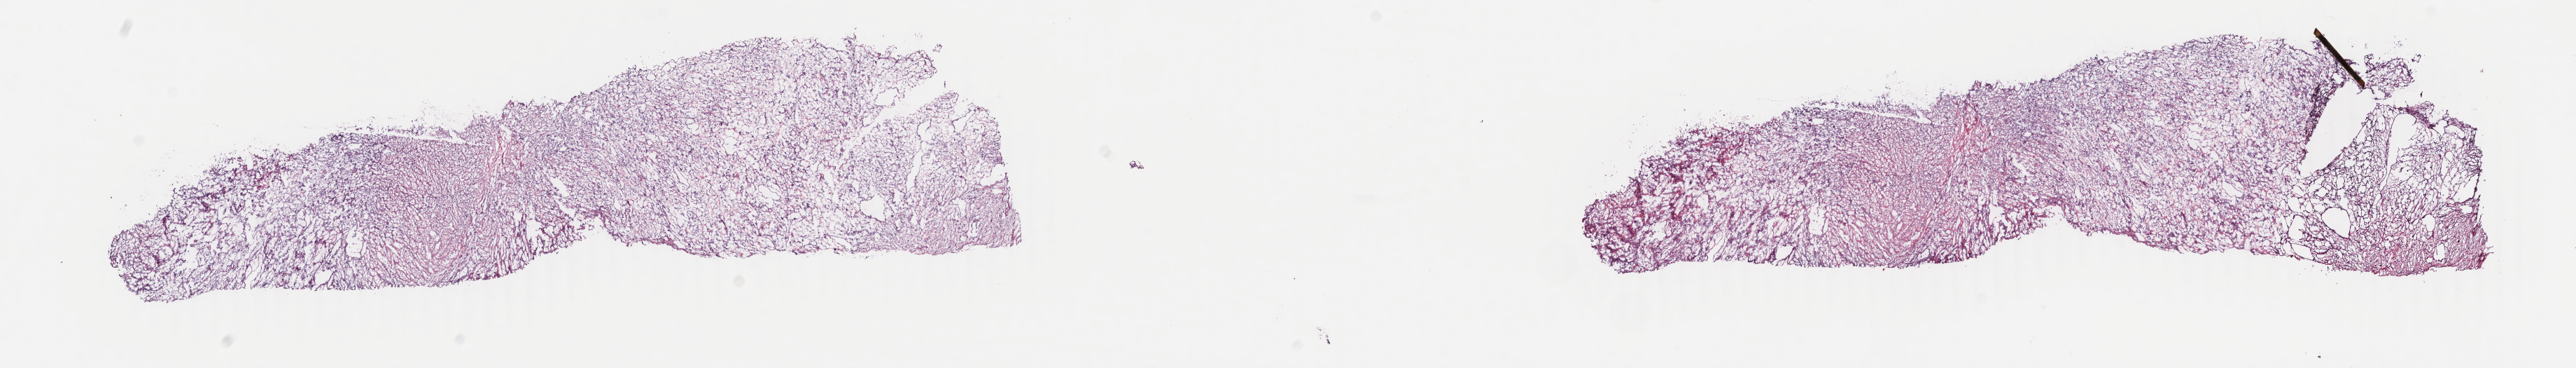
Digitized H&E-stained tissue section (whole slide), a low-resolution overview of the entire scanned area, about 29.3 x 4.2 mm, frozen section, sample: primary tumour, retroperitoneum and peritoneum. Patient: male, age at initial diagnosis 51 years. Pathologist review of this section (percent, as recorded): tumour cells 100%, tumour nuclei 75%, normal cells 0%, stromal cells 0%, necrosis 0%. Inflammatory infiltration, as recorded: lymphocyte infiltration 1%, monocyte infiltration 0%, neutrophil infiltration 0%.
Pathologic diagnosis: Dedifferentiated liposarcoma (retroperitoneum).